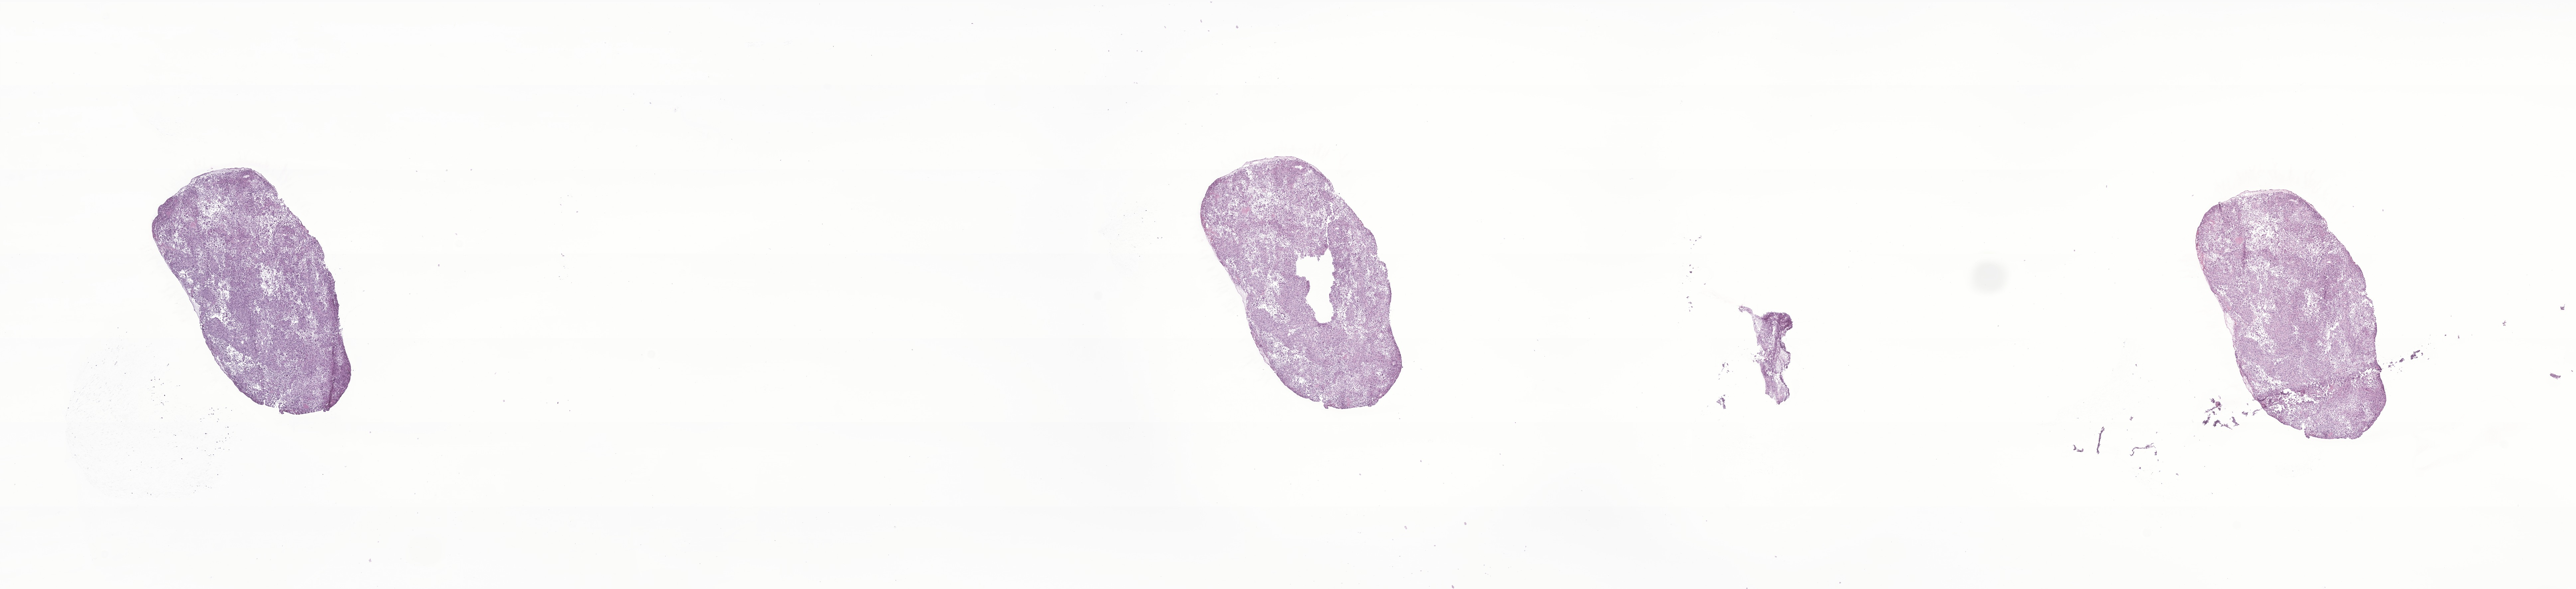
Hematoxylin and eosin (H&E) whole-slide image of tumor tissue from the brain, a low-resolution overview of the entire scanned area, about 32.7 x 7.5 mm, frozen section (OCT-embedded). Patient: male, age 165 months (13 years 9 months).
- diagnosis: Glioma, malignant